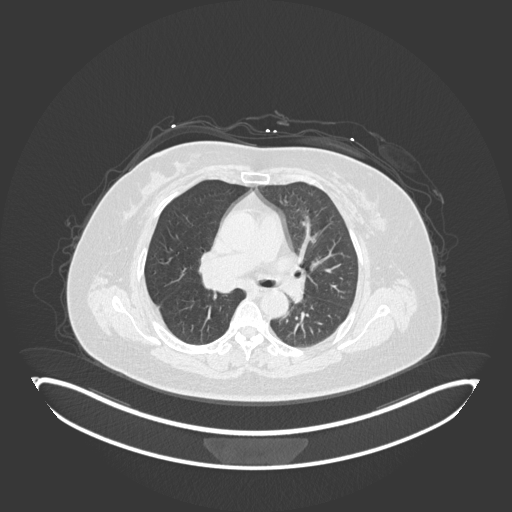
Chest CT, one axial slice. Position 98 of 245 along the scan axis. Reconstruction kernel B30f. Lung window (W 1500 / L -600 HU). 1 mm slice thickness. 512 × 512 image matrix, field of view 500 × 500 mm. Patient: female, 60 years. Case-level facts recorded for this patient, not image findings: clinical TNM (as recorded): T1c N0 M0; histopathological grade: G1-G2.
Outlined on this slice (rectangle marked by the reading radiologist):
- lung tumour (recorded histology: squamous cell carcinoma): bounding box [x1, y1, x2, y2] px = [201, 272, 240, 297]